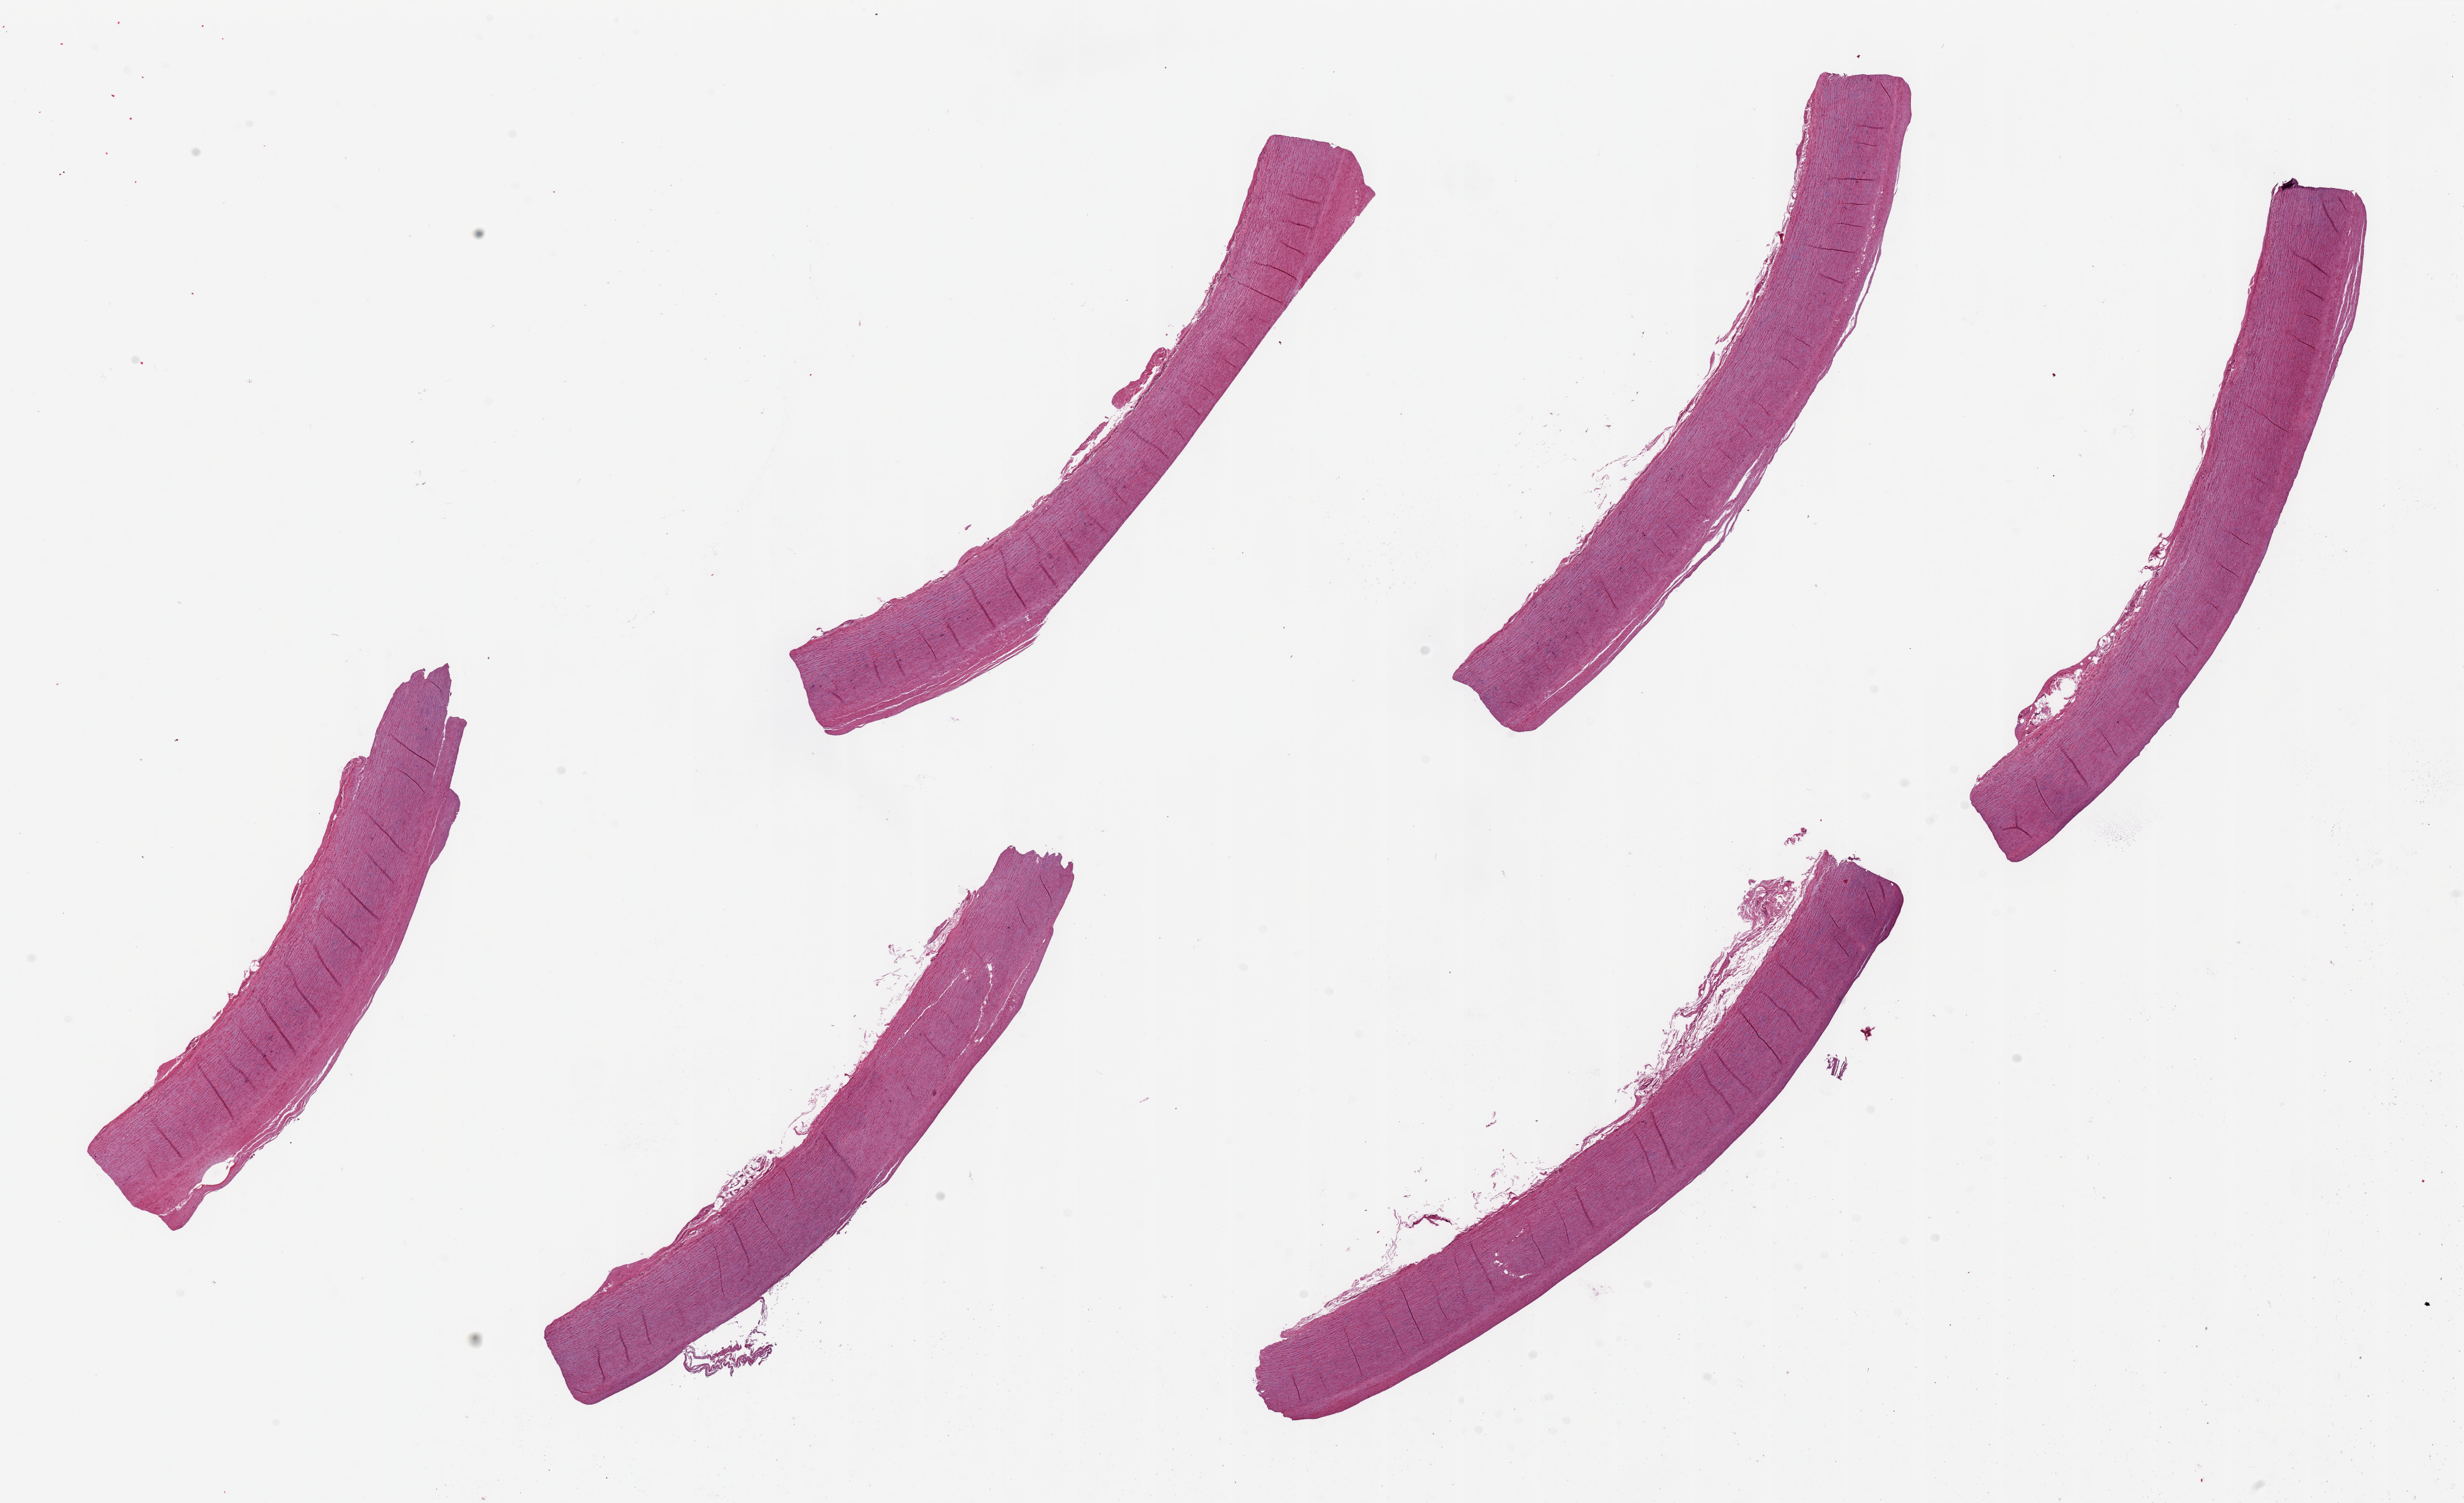
Digitized H&E-stained section, brightfield, low-resolution overview of the scanned area, about 31.5 x 19.2 mm. PAXgene-fixed paraffin-embedded (PFPE) section. Target tissue: aorta. Donor tissue sample. Female donor.
Reviewer comment on this tissue sample: 6 pieces~10 x 1mm.